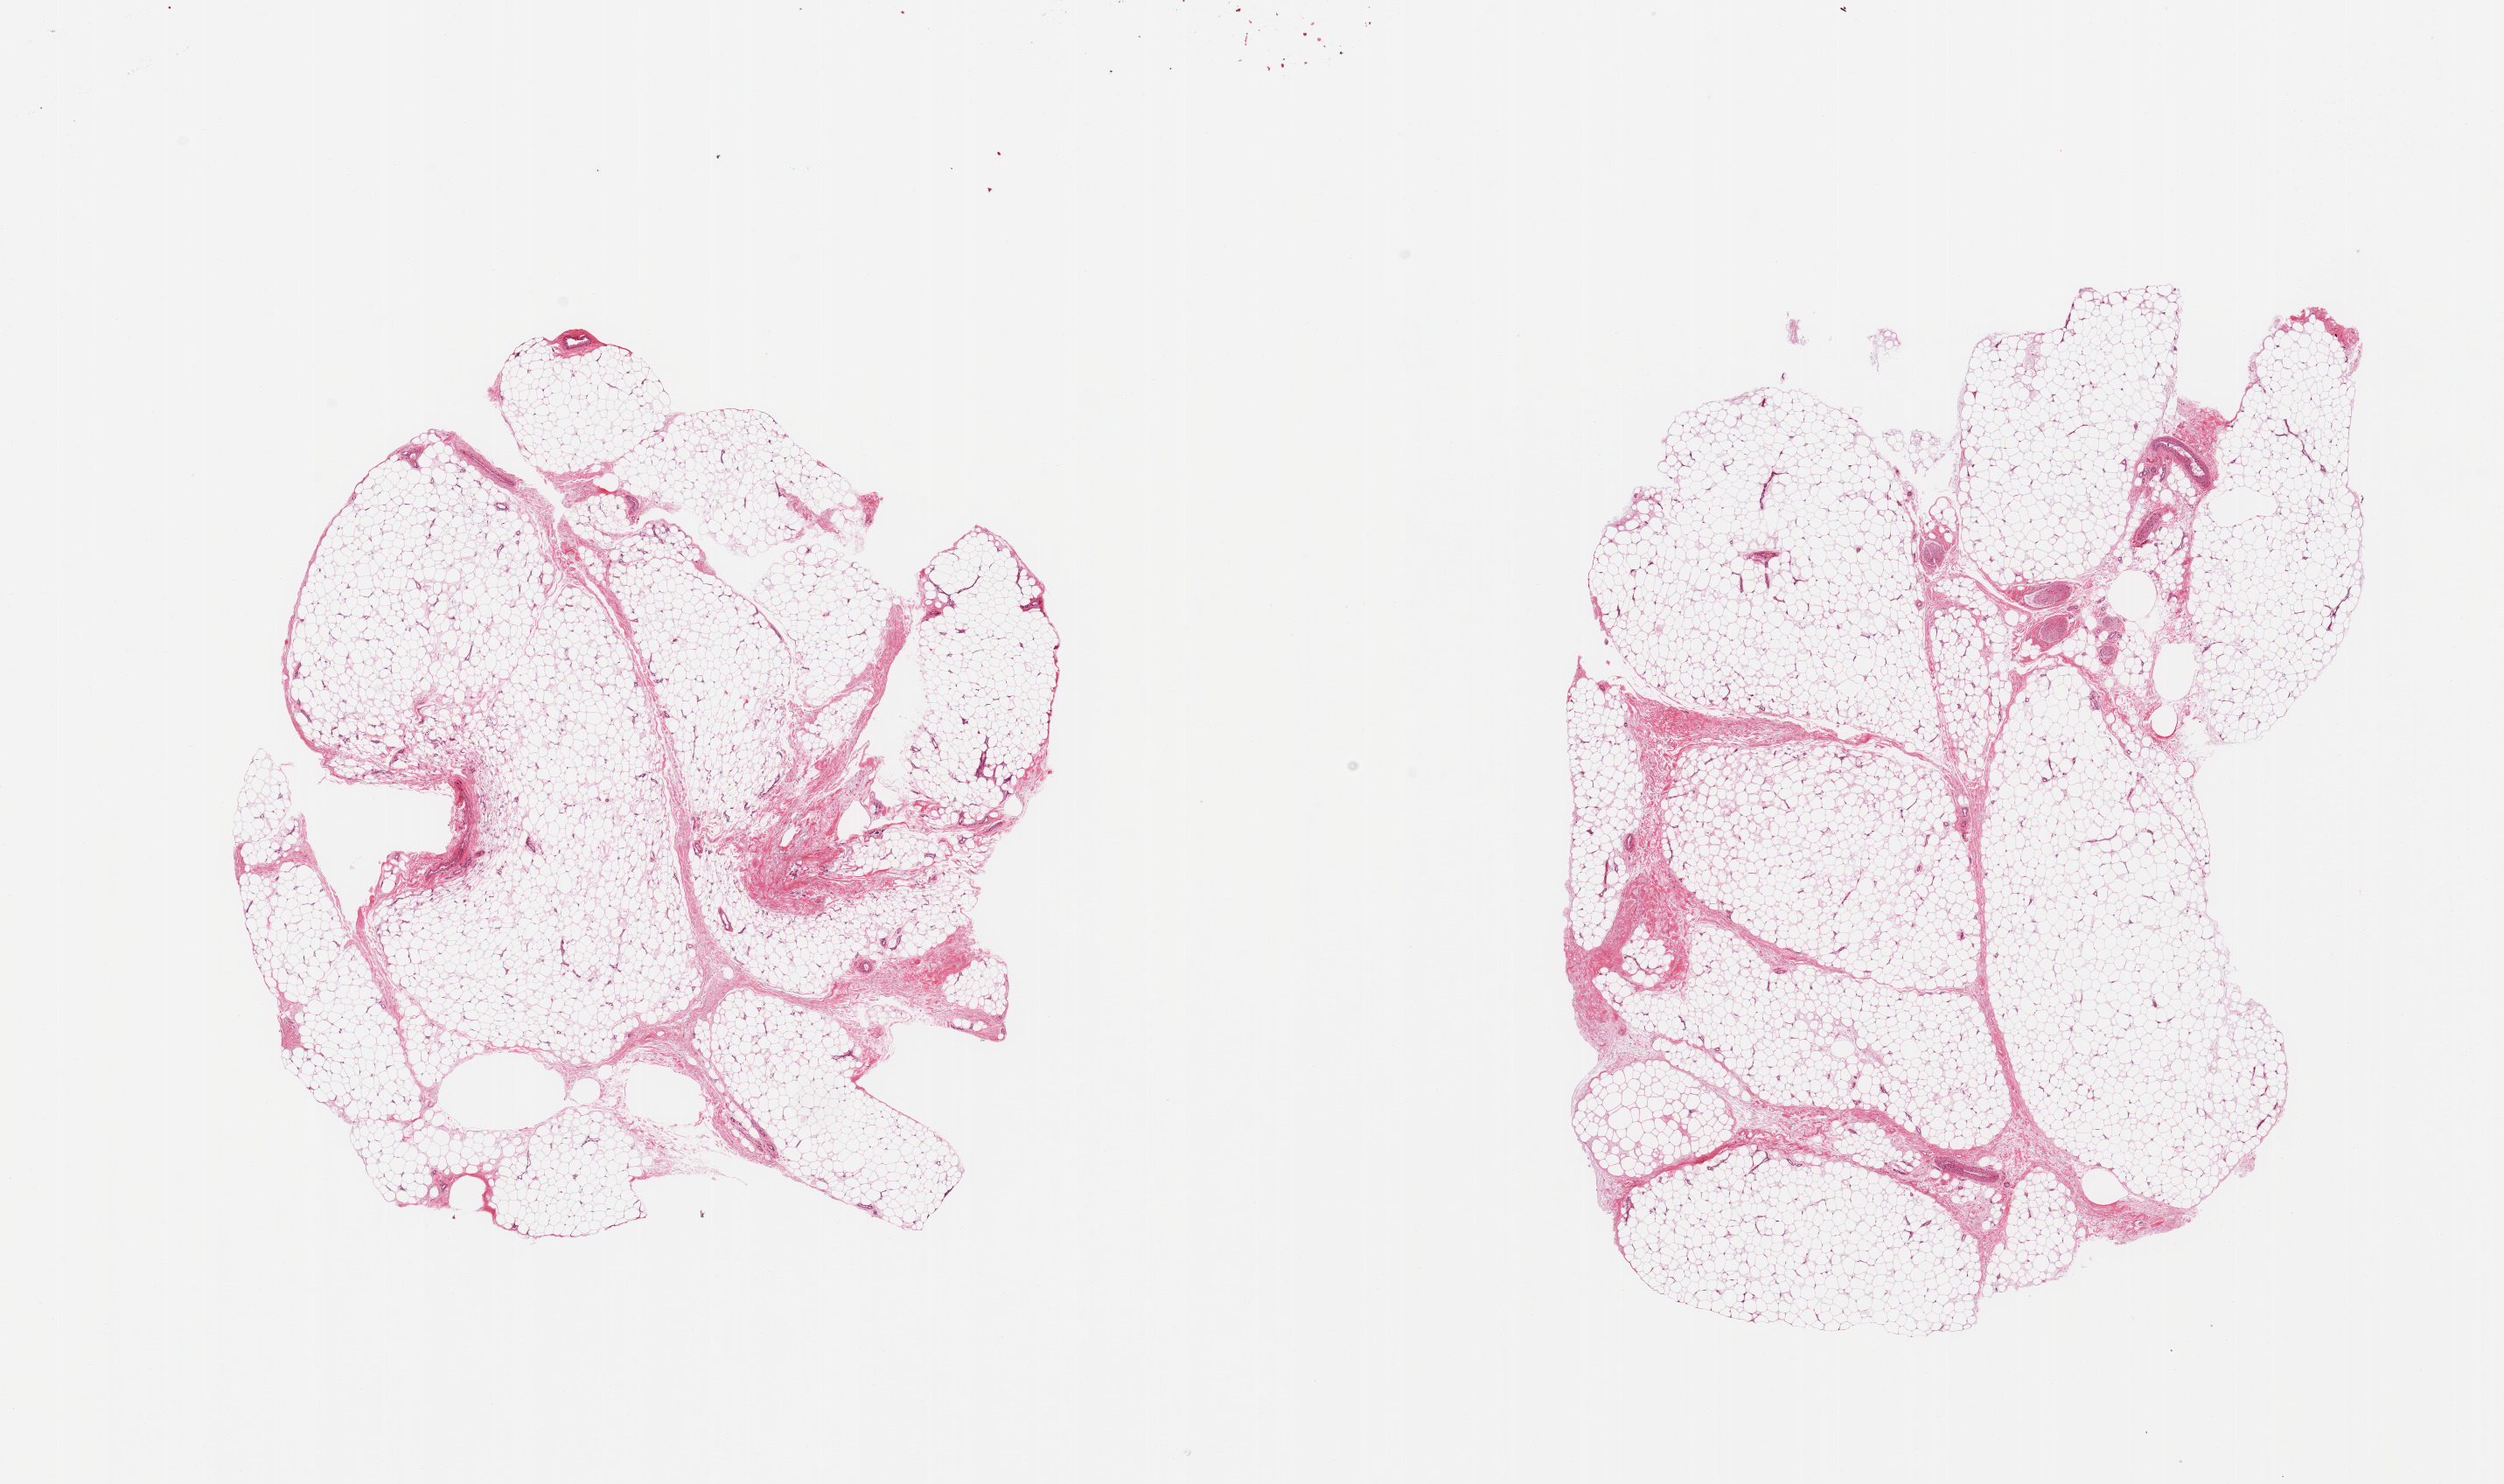
Hematoxylin and eosin (H&E) whole-slide image, shown as a low-resolution overview of the whole scanned area (about 22.6 x 13.4 mm); PAXgene-fixed, paraffin-embedded tissue; section of adipose tissue (target tissue); tissue donor sample. Donor sex: male.
Review note (as recorded): 2 pieces; mature fat, <10% fibrous tissue and nerve.